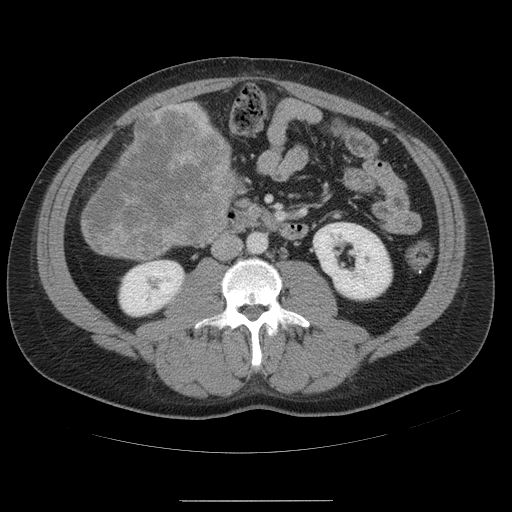
Contrast-enhanced abdominal CT, one axial slice; intravenous contrast given; soft-tissue window (W 400 / L 40 HU); 5 mm slice thickness; 512 × 512 image matrix, field of view 436 × 436 mm. Male patient, age 40 years. From the clinical record (not read from this slice): diagnosis: colorectal cancer liver metastases, imaged before liver resection; multiple liver metastases: no; largest metastasis: 15 cm.
Outlined on this slice (manually delineated by an expert):
- liver: bounding box <82,102,239,262> (left, top, right, bottom; pixels)
- liver metastasis: <82,110,234,260>